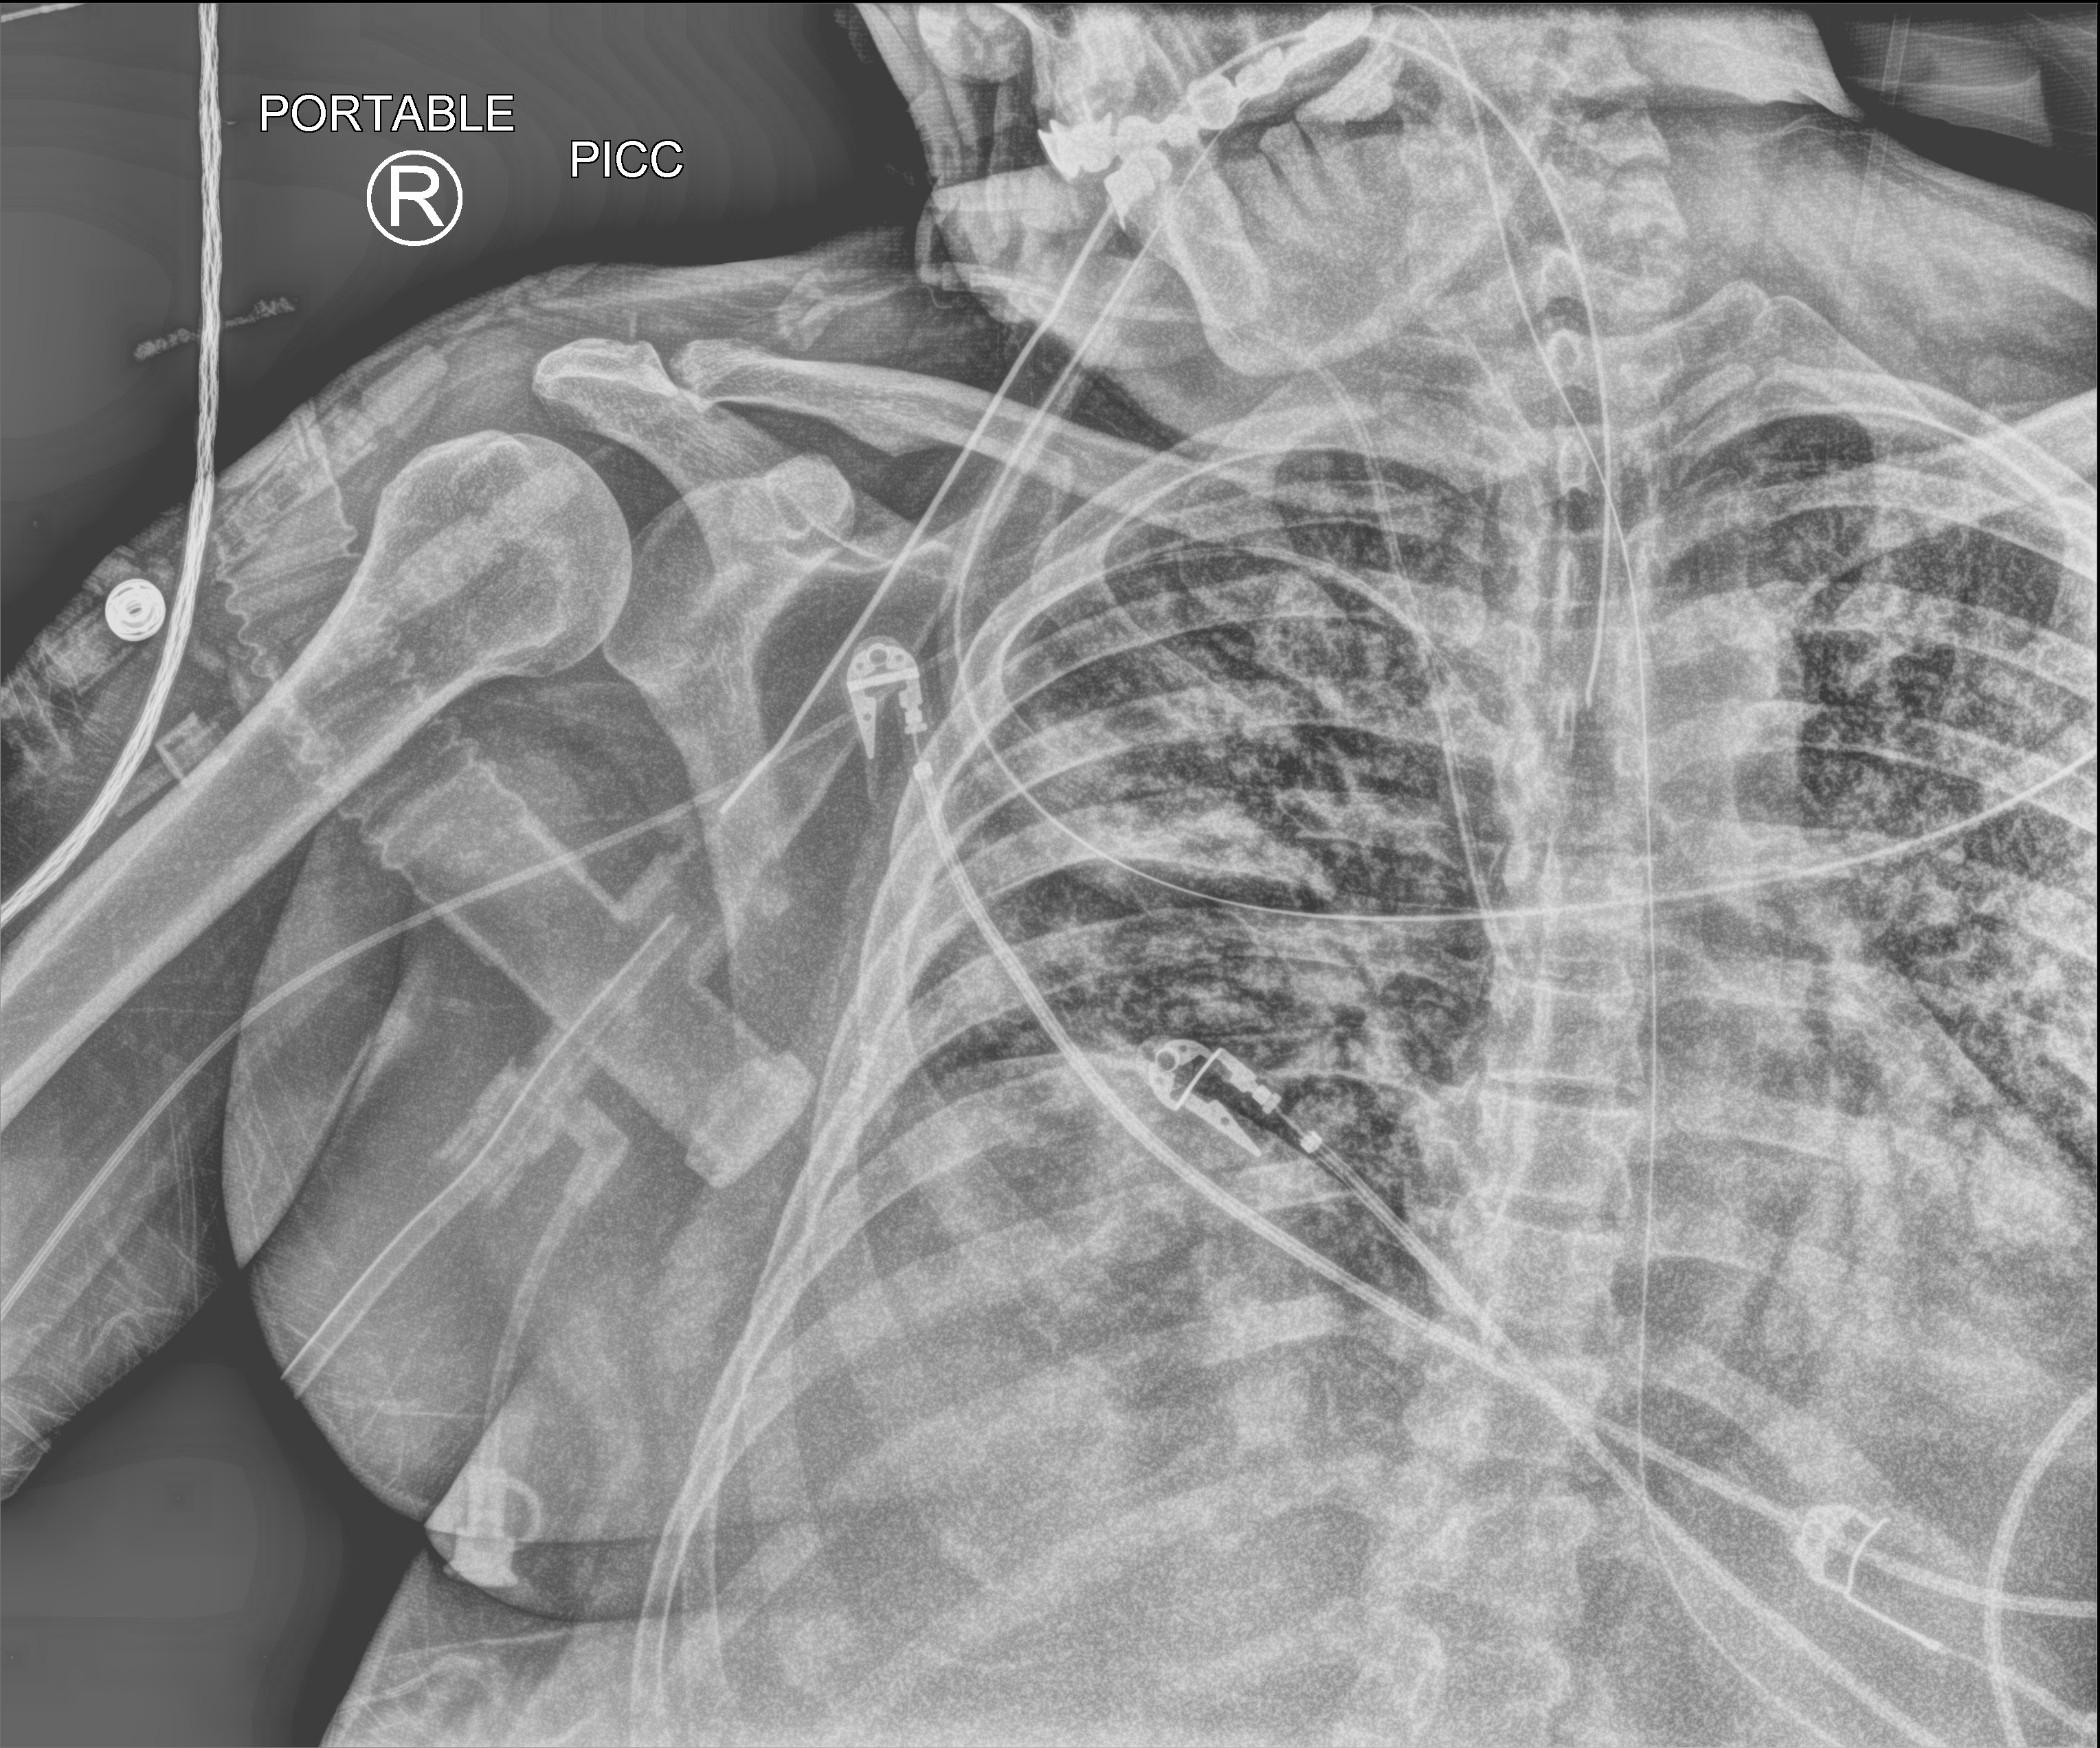
Portable chest radiograph, anteroposterior (AP) projection. Male patient hospitalised with COVID-19, age 18–59 years.
From the hospital-stay record, not from the radiograph (when in the stay this image was taken is not recorded): admitted to intensive care during this hospital stay: yes.